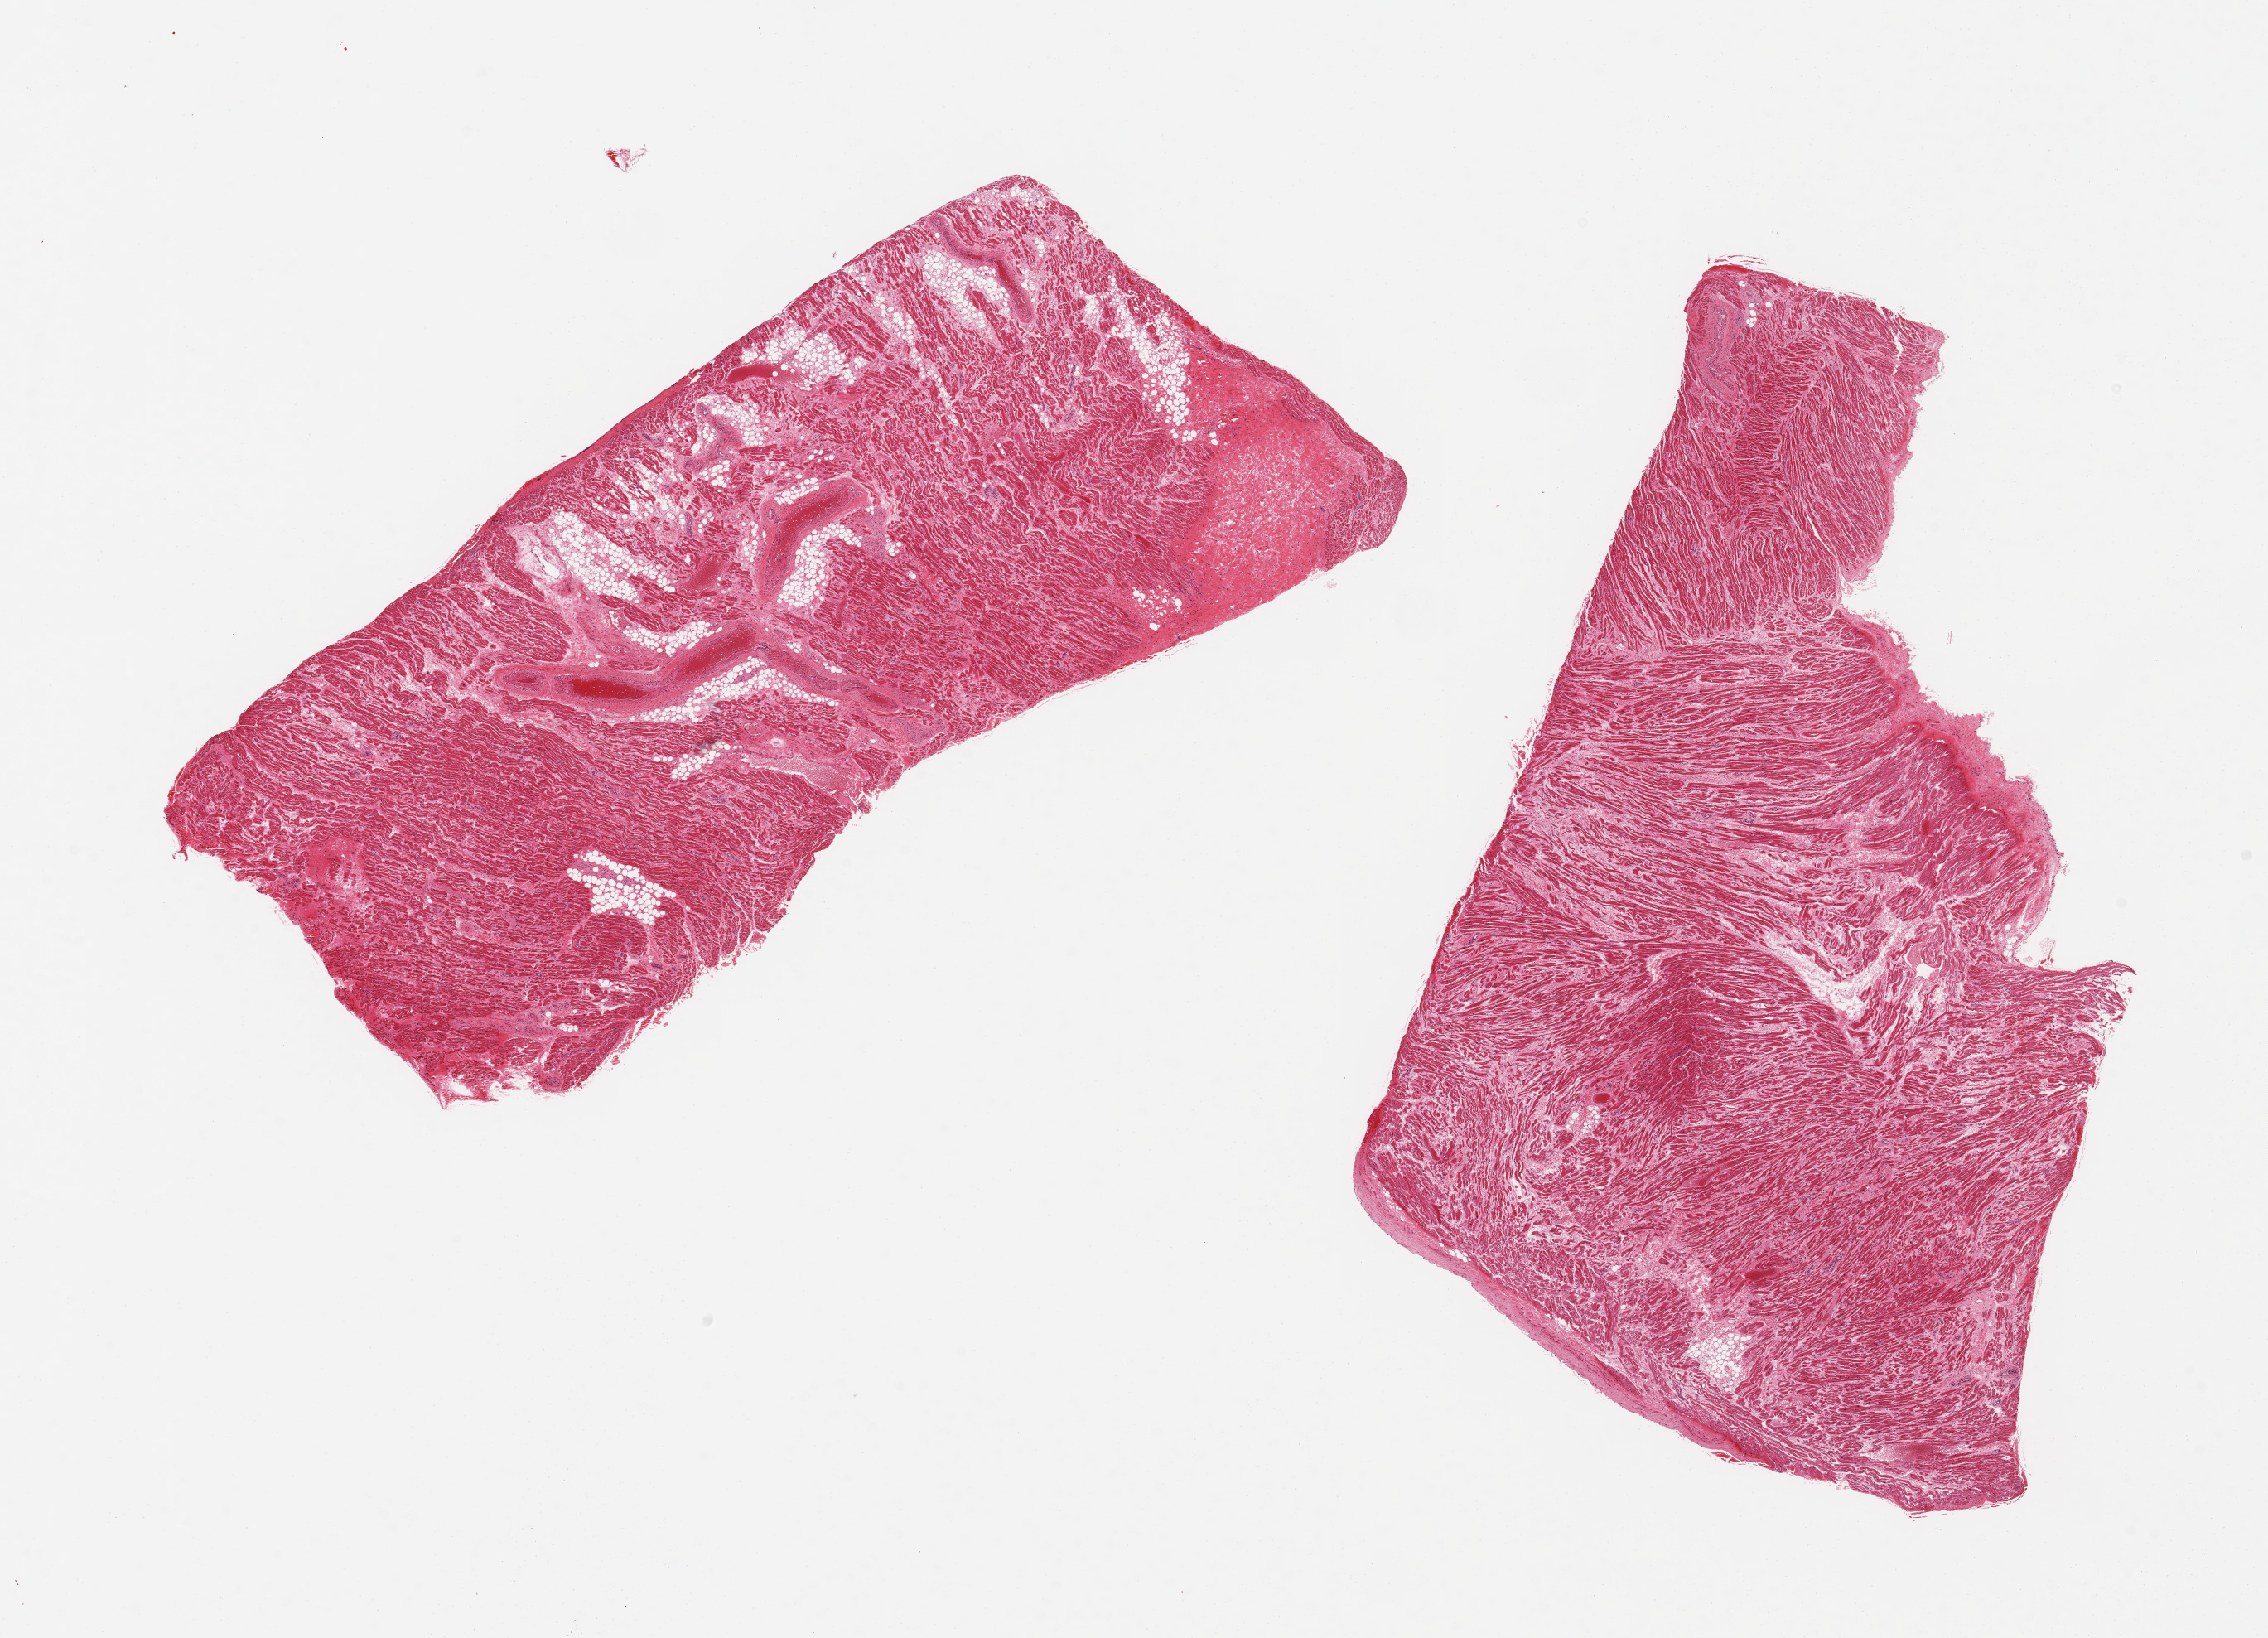
Digitized hematoxylin and eosin (H&E)-stained section, shown as a low-resolution overview of the whole scanned area (about 21.7 x 15.6 mm, from a 20x scan), PAXgene-fixed paraffin-embedded (PFPE) section, target tissue: auricular appendage, donor tissue sample. Male donor.
Pathologist's review note for this sample: 2 pieces; 1 has 20% internal fat.